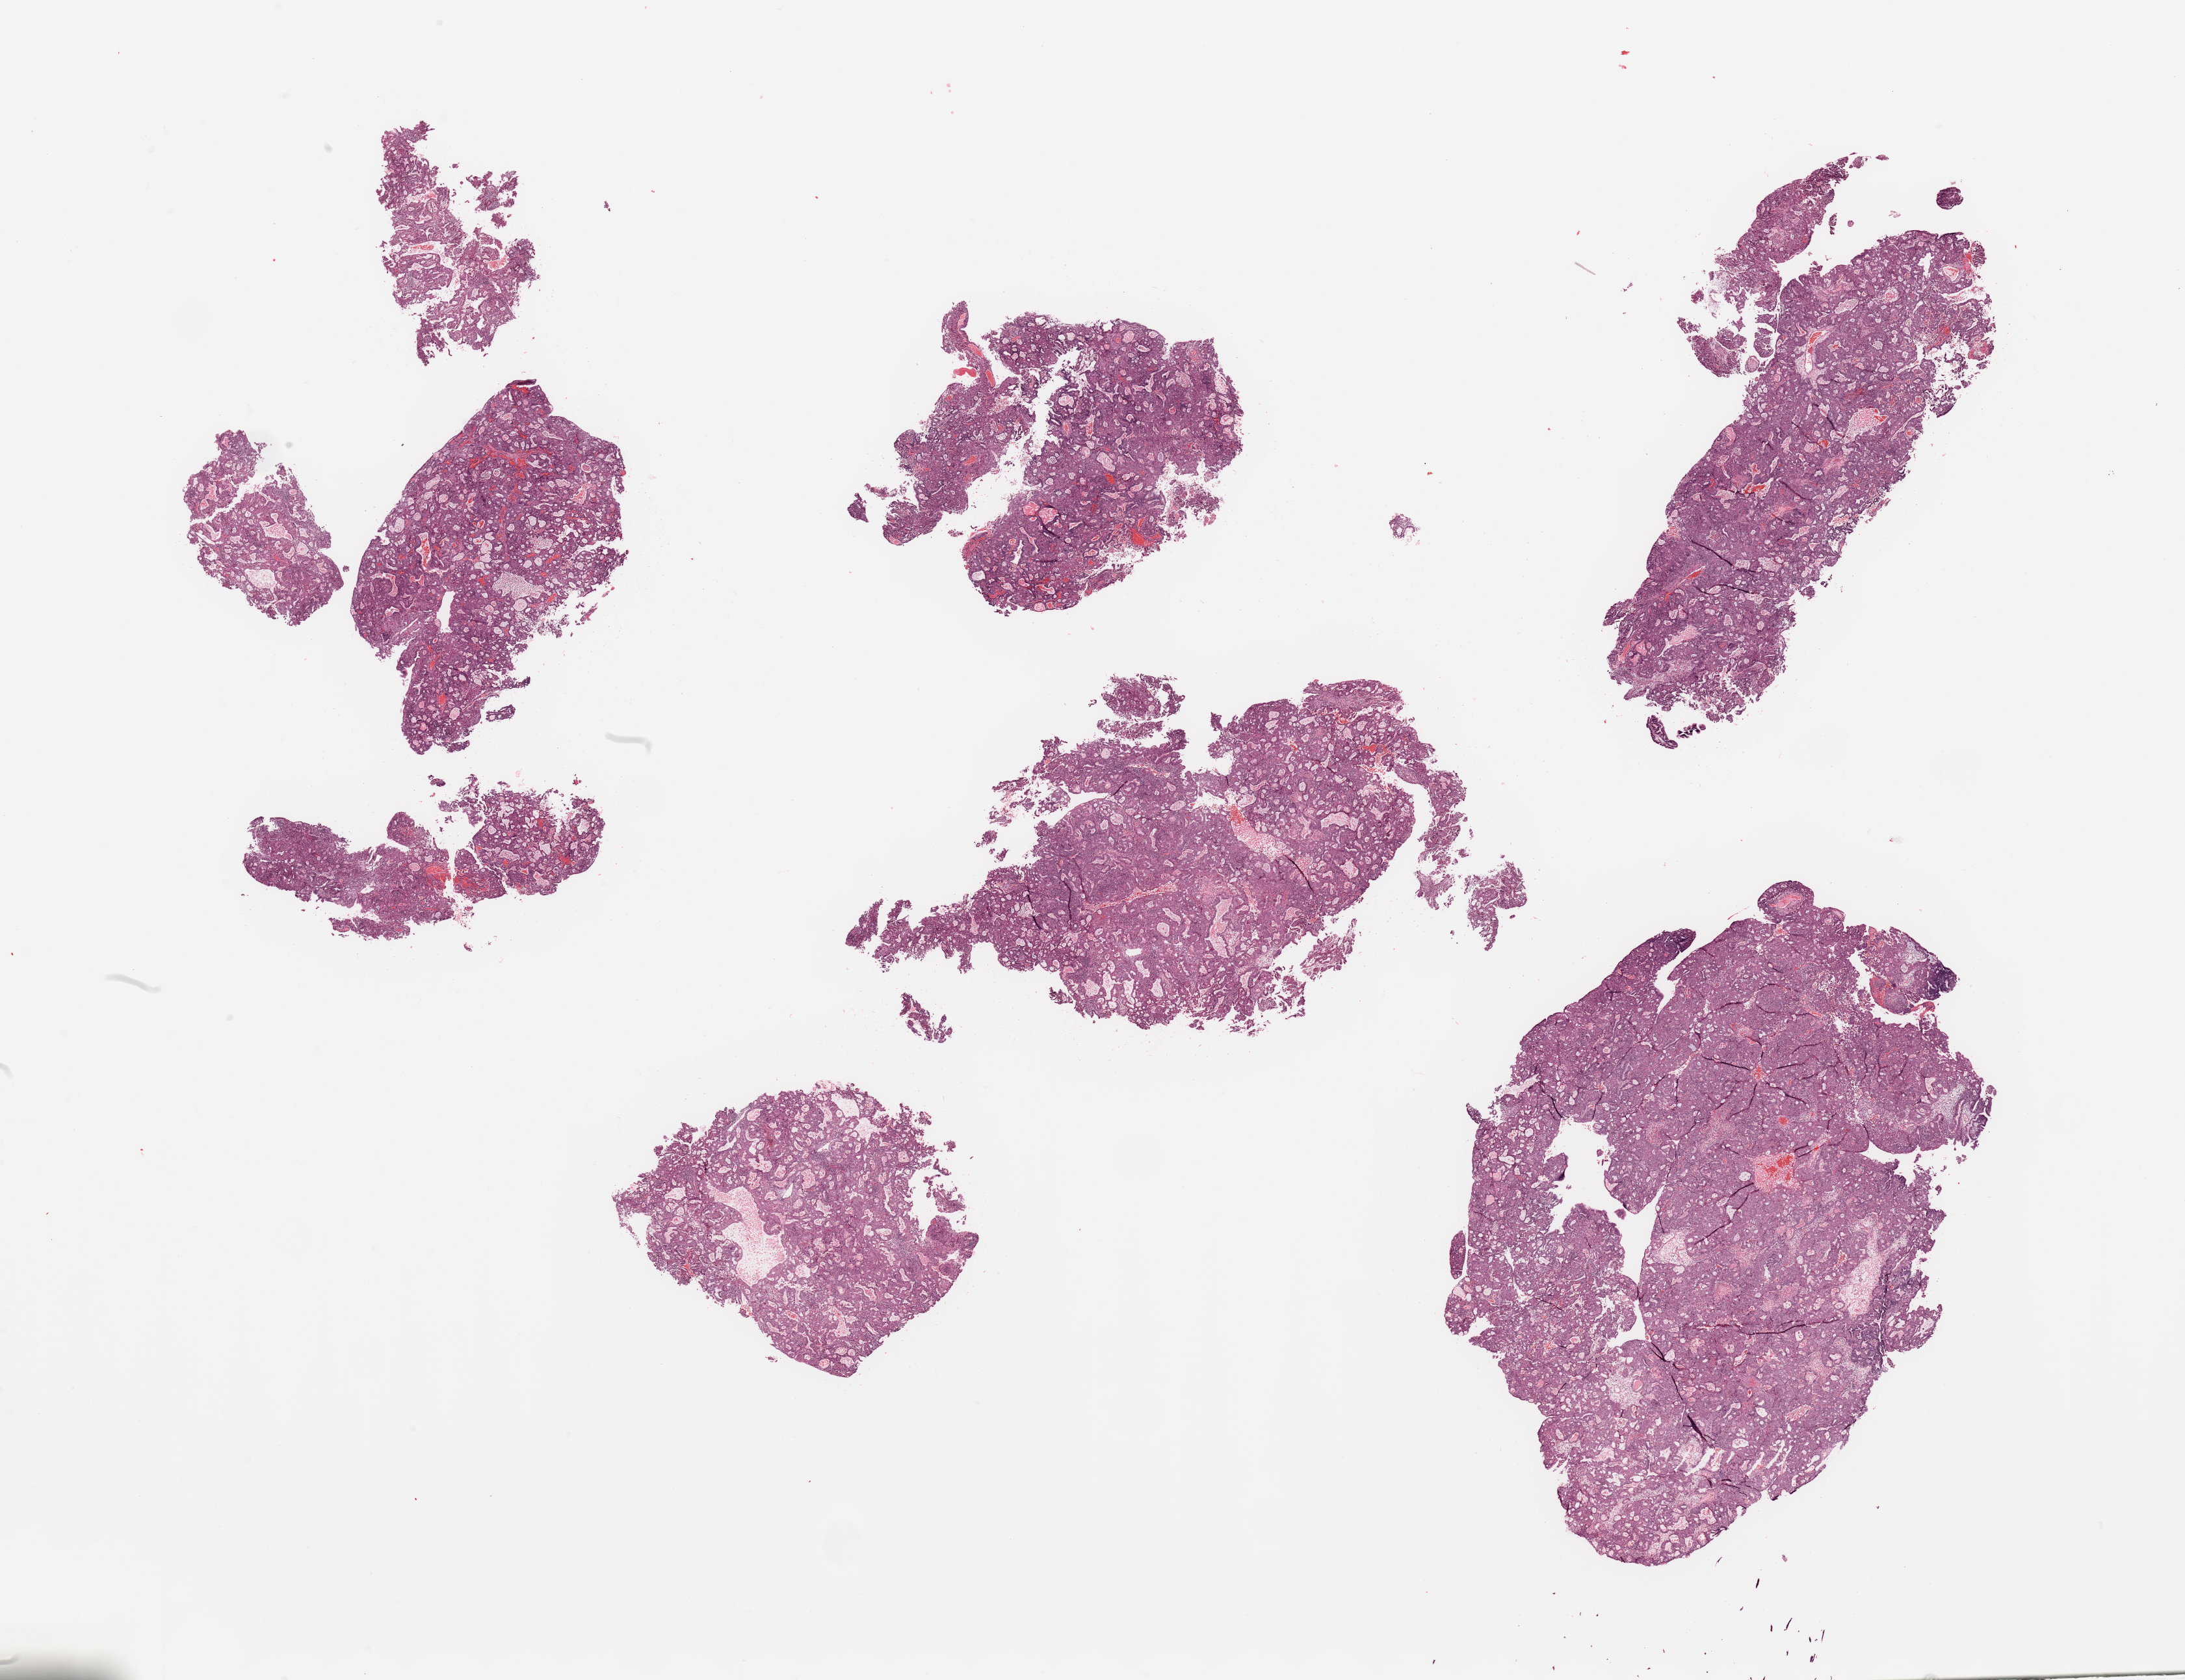
H&E-stained whole-slide image — shown as a low-resolution overview of the whole scanned area (about 26.6 x 20.4 mm). Tumour tissue sample, uterus. Female, 60 y/o.
Histologic diagnosis: Endometrioid adenocarcinoma, NOS.